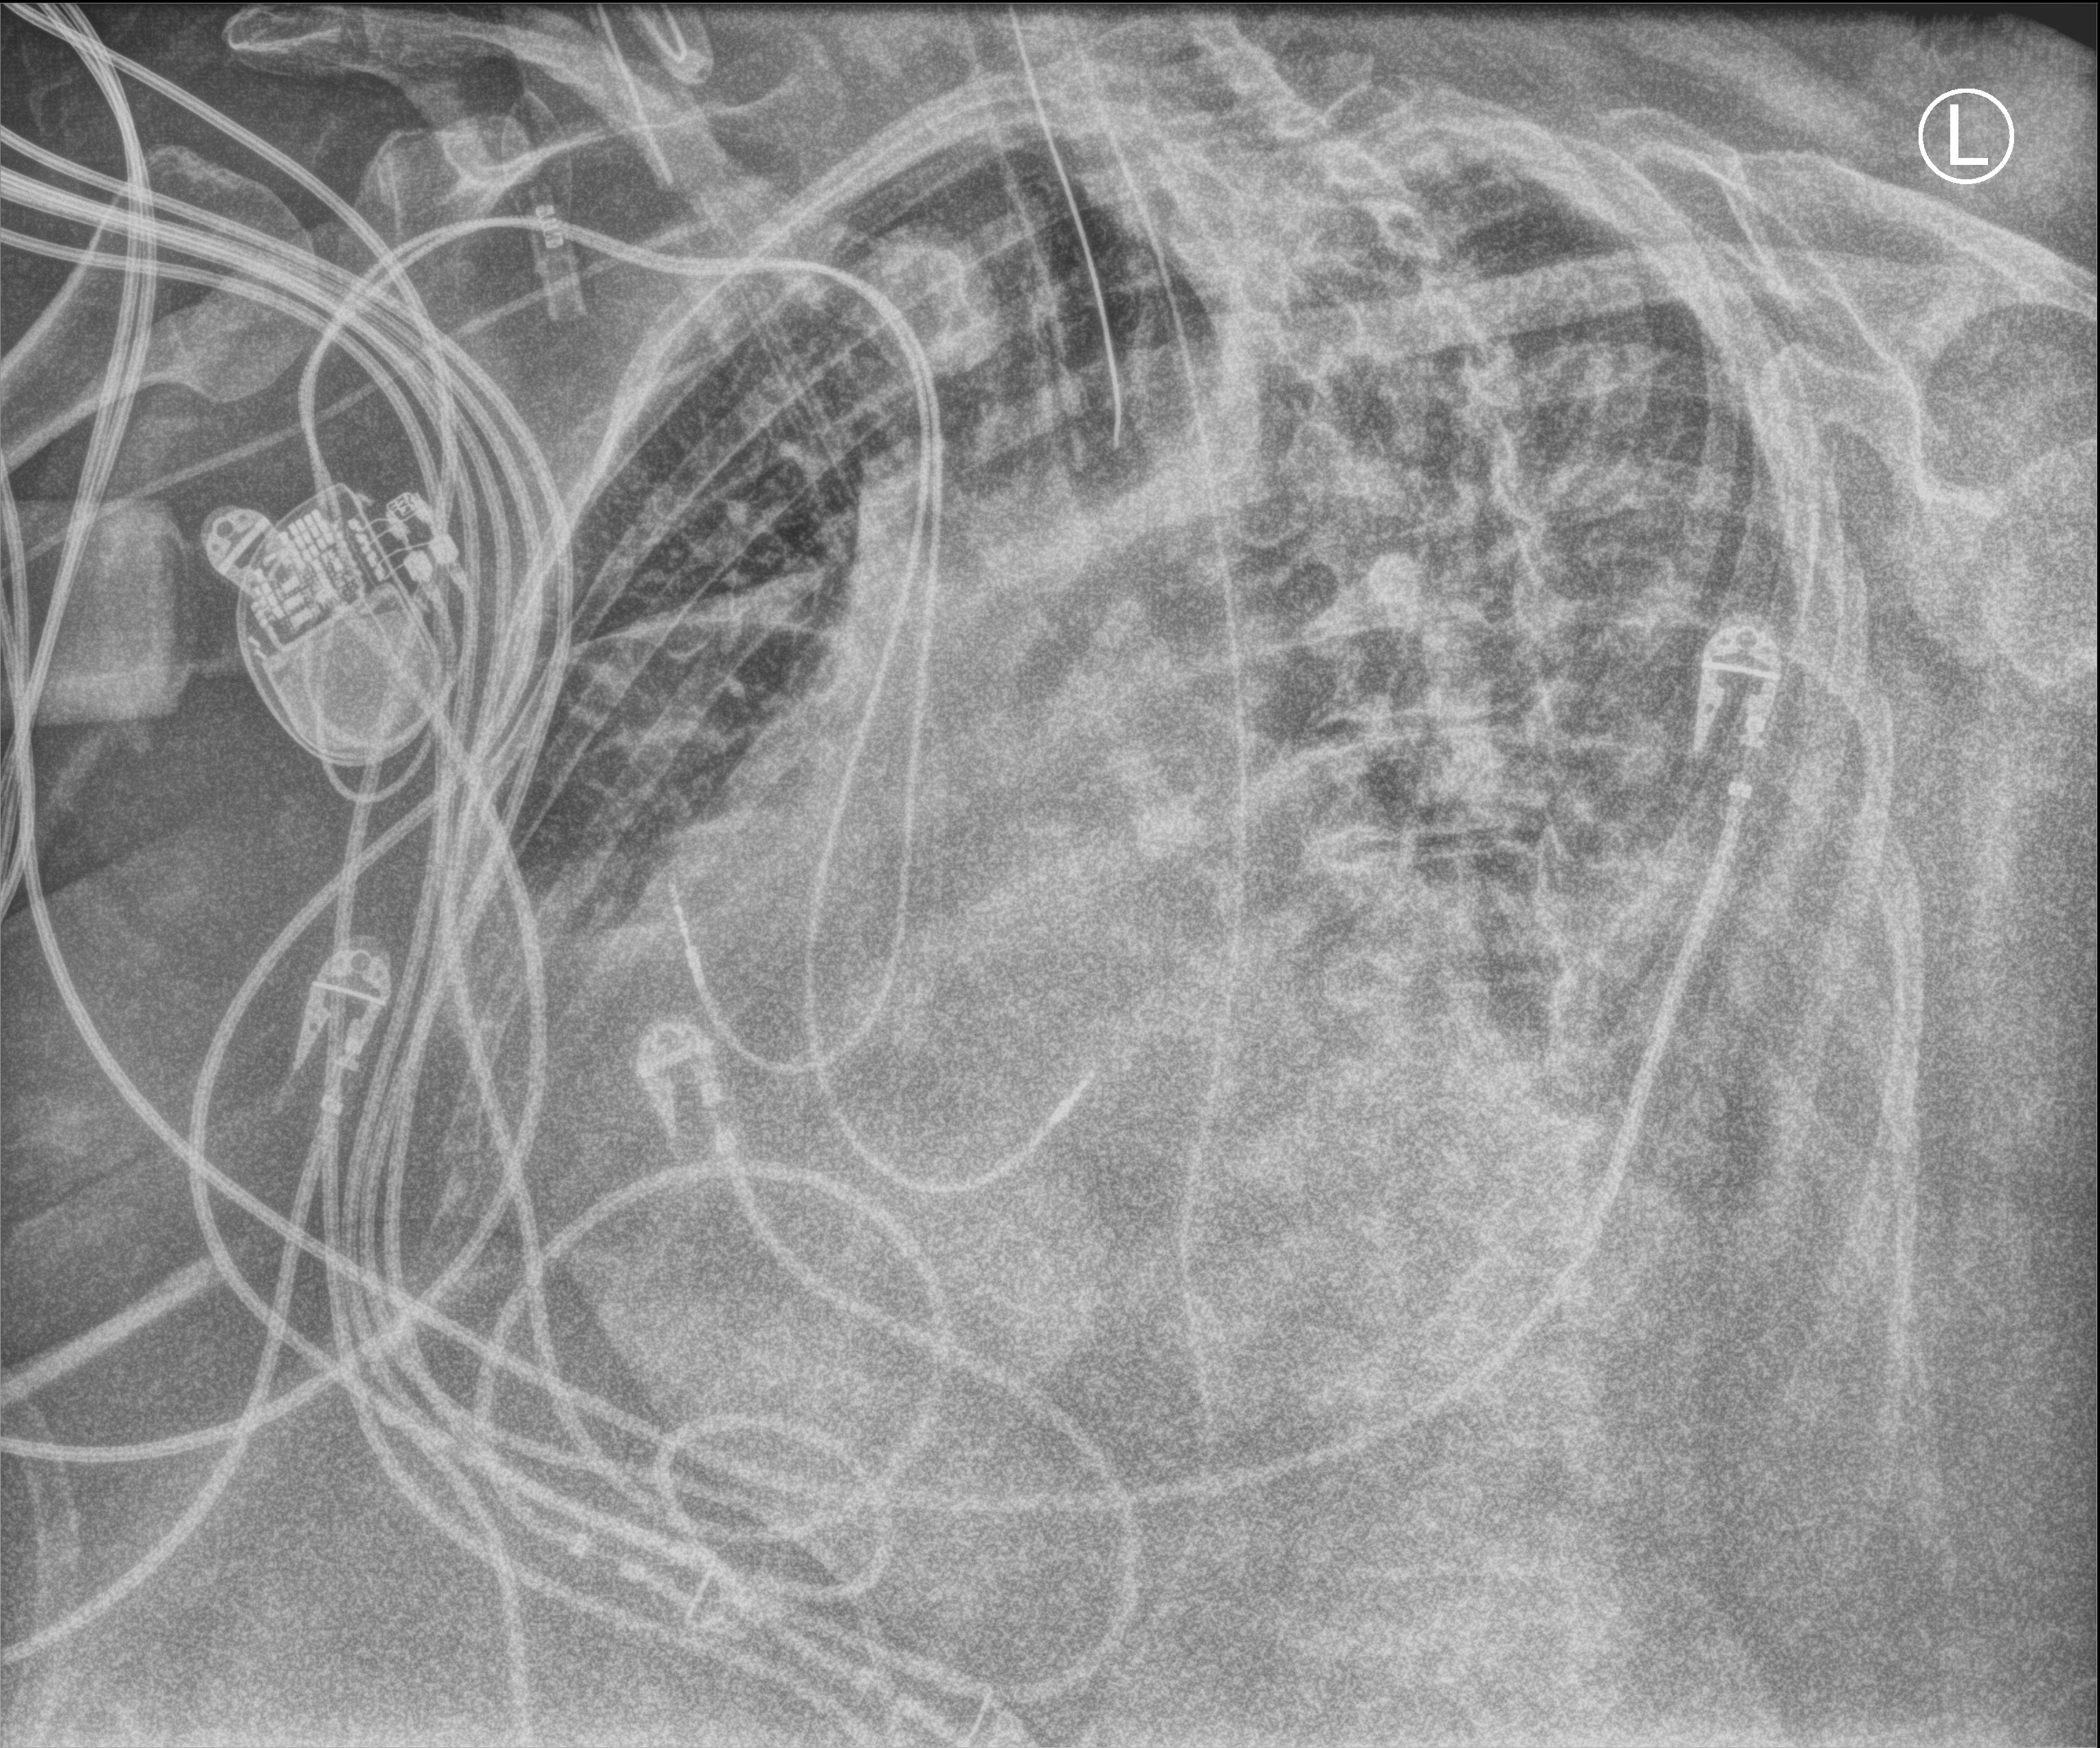
Portable chest radiograph; anteroposterior (AP) projection. Female patient hospitalised with COVID-19, age 75–90 years.
From the hospital-stay record, not from the radiograph (when in the stay this image was taken is not recorded): length of hospital stay: 21 days; admitted to intensive care during this hospital stay: yes; other chronic lung disease (admission record): yes.